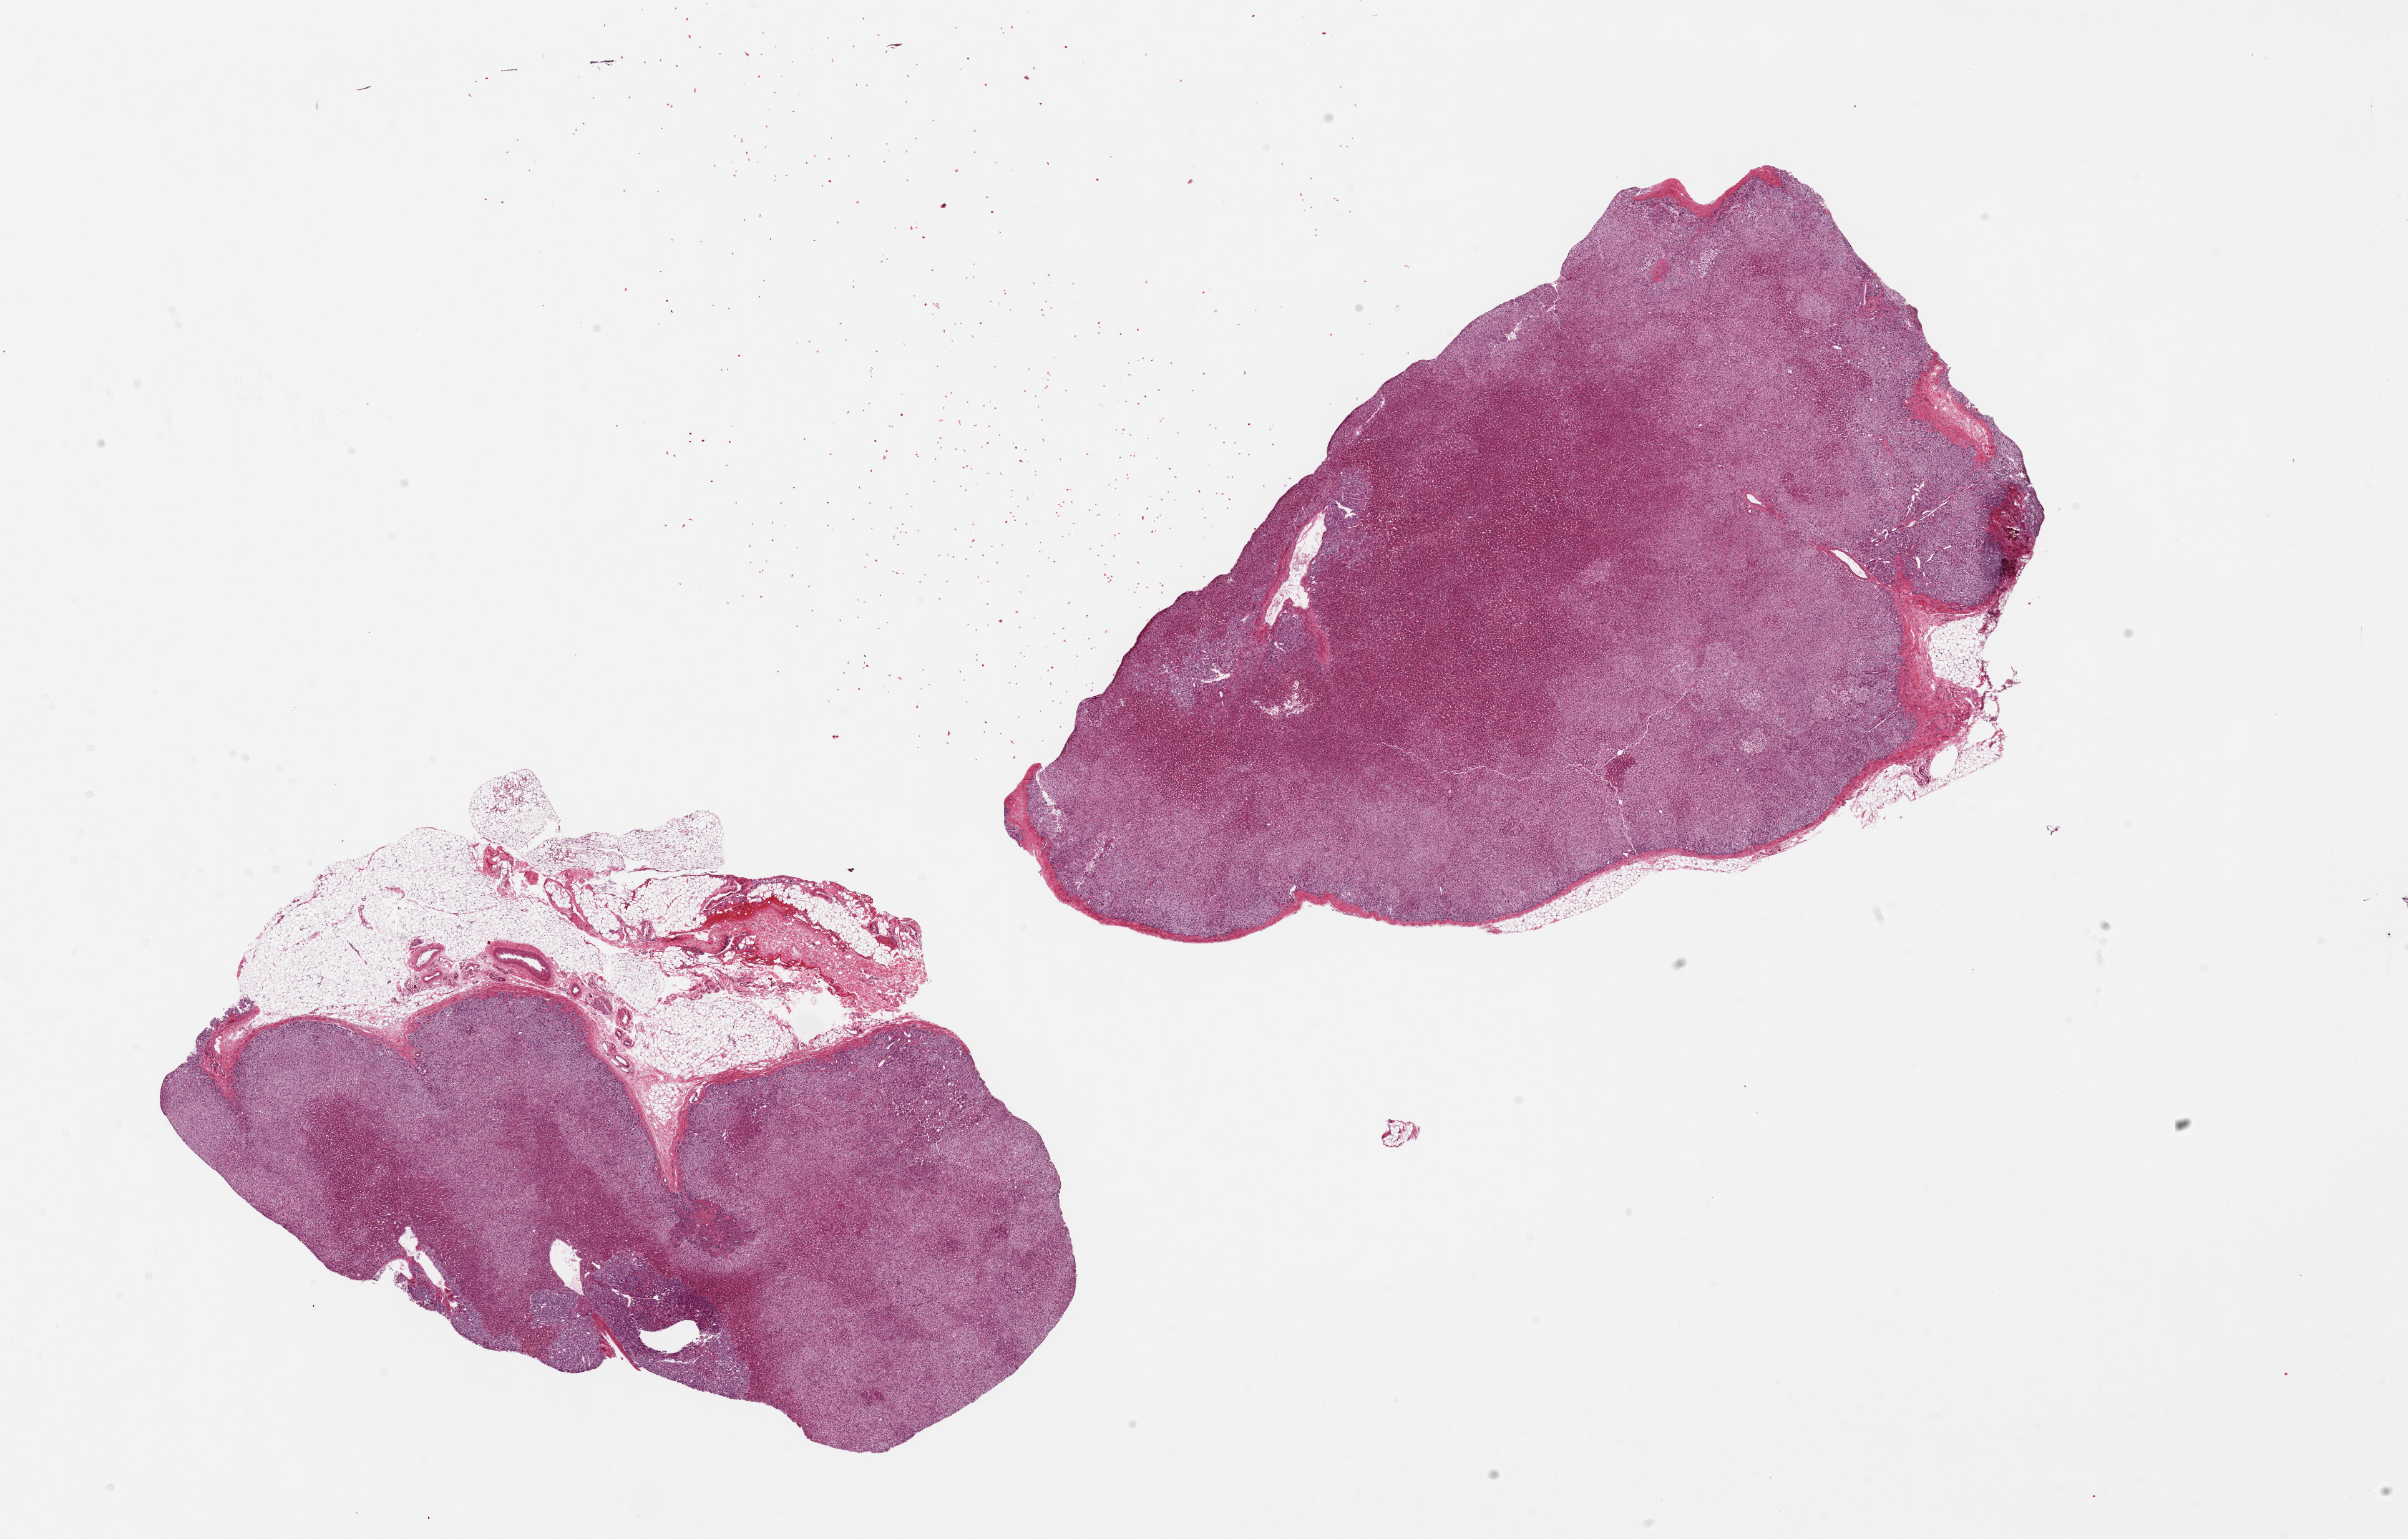
Digitized haematoxylin and eosin-stained section — a low-resolution overview of the entire scanned area, about 30.5 x 19.5 mm. PAXgene-fixed paraffin-embedded (PFPE) section. Target tissue: adrenal gland. Tissue donor sample. Female donor.
* review note (as recorded): 2 pieces. 11.5x8 & 13x9mm; Smaller piece is 40% adipose